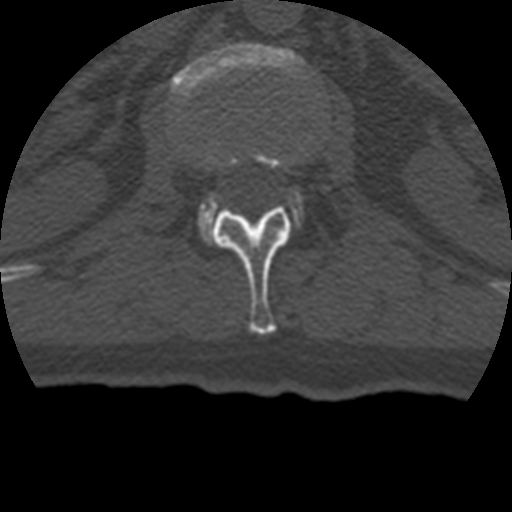
CT including the spine, one axial slice. Reconstruction kernel STANDARD. 120 kVp. Bone window (W 1800 / L 400 HU). 1.25 mm slice thickness. 512 × 512 image matrix. Patient age 69 years. Case-level facts recorded for this patient, not image findings: primary cancer: prostate.
Structures marked on this image (semi-automatic segmentation, software-assisted and operator-edited):
- L1 vertebra: bounding box (x1, y1, x2, y2) in pixels: (212, 148, 295, 334)
- L2 vertebra: (171, 43, 314, 239)